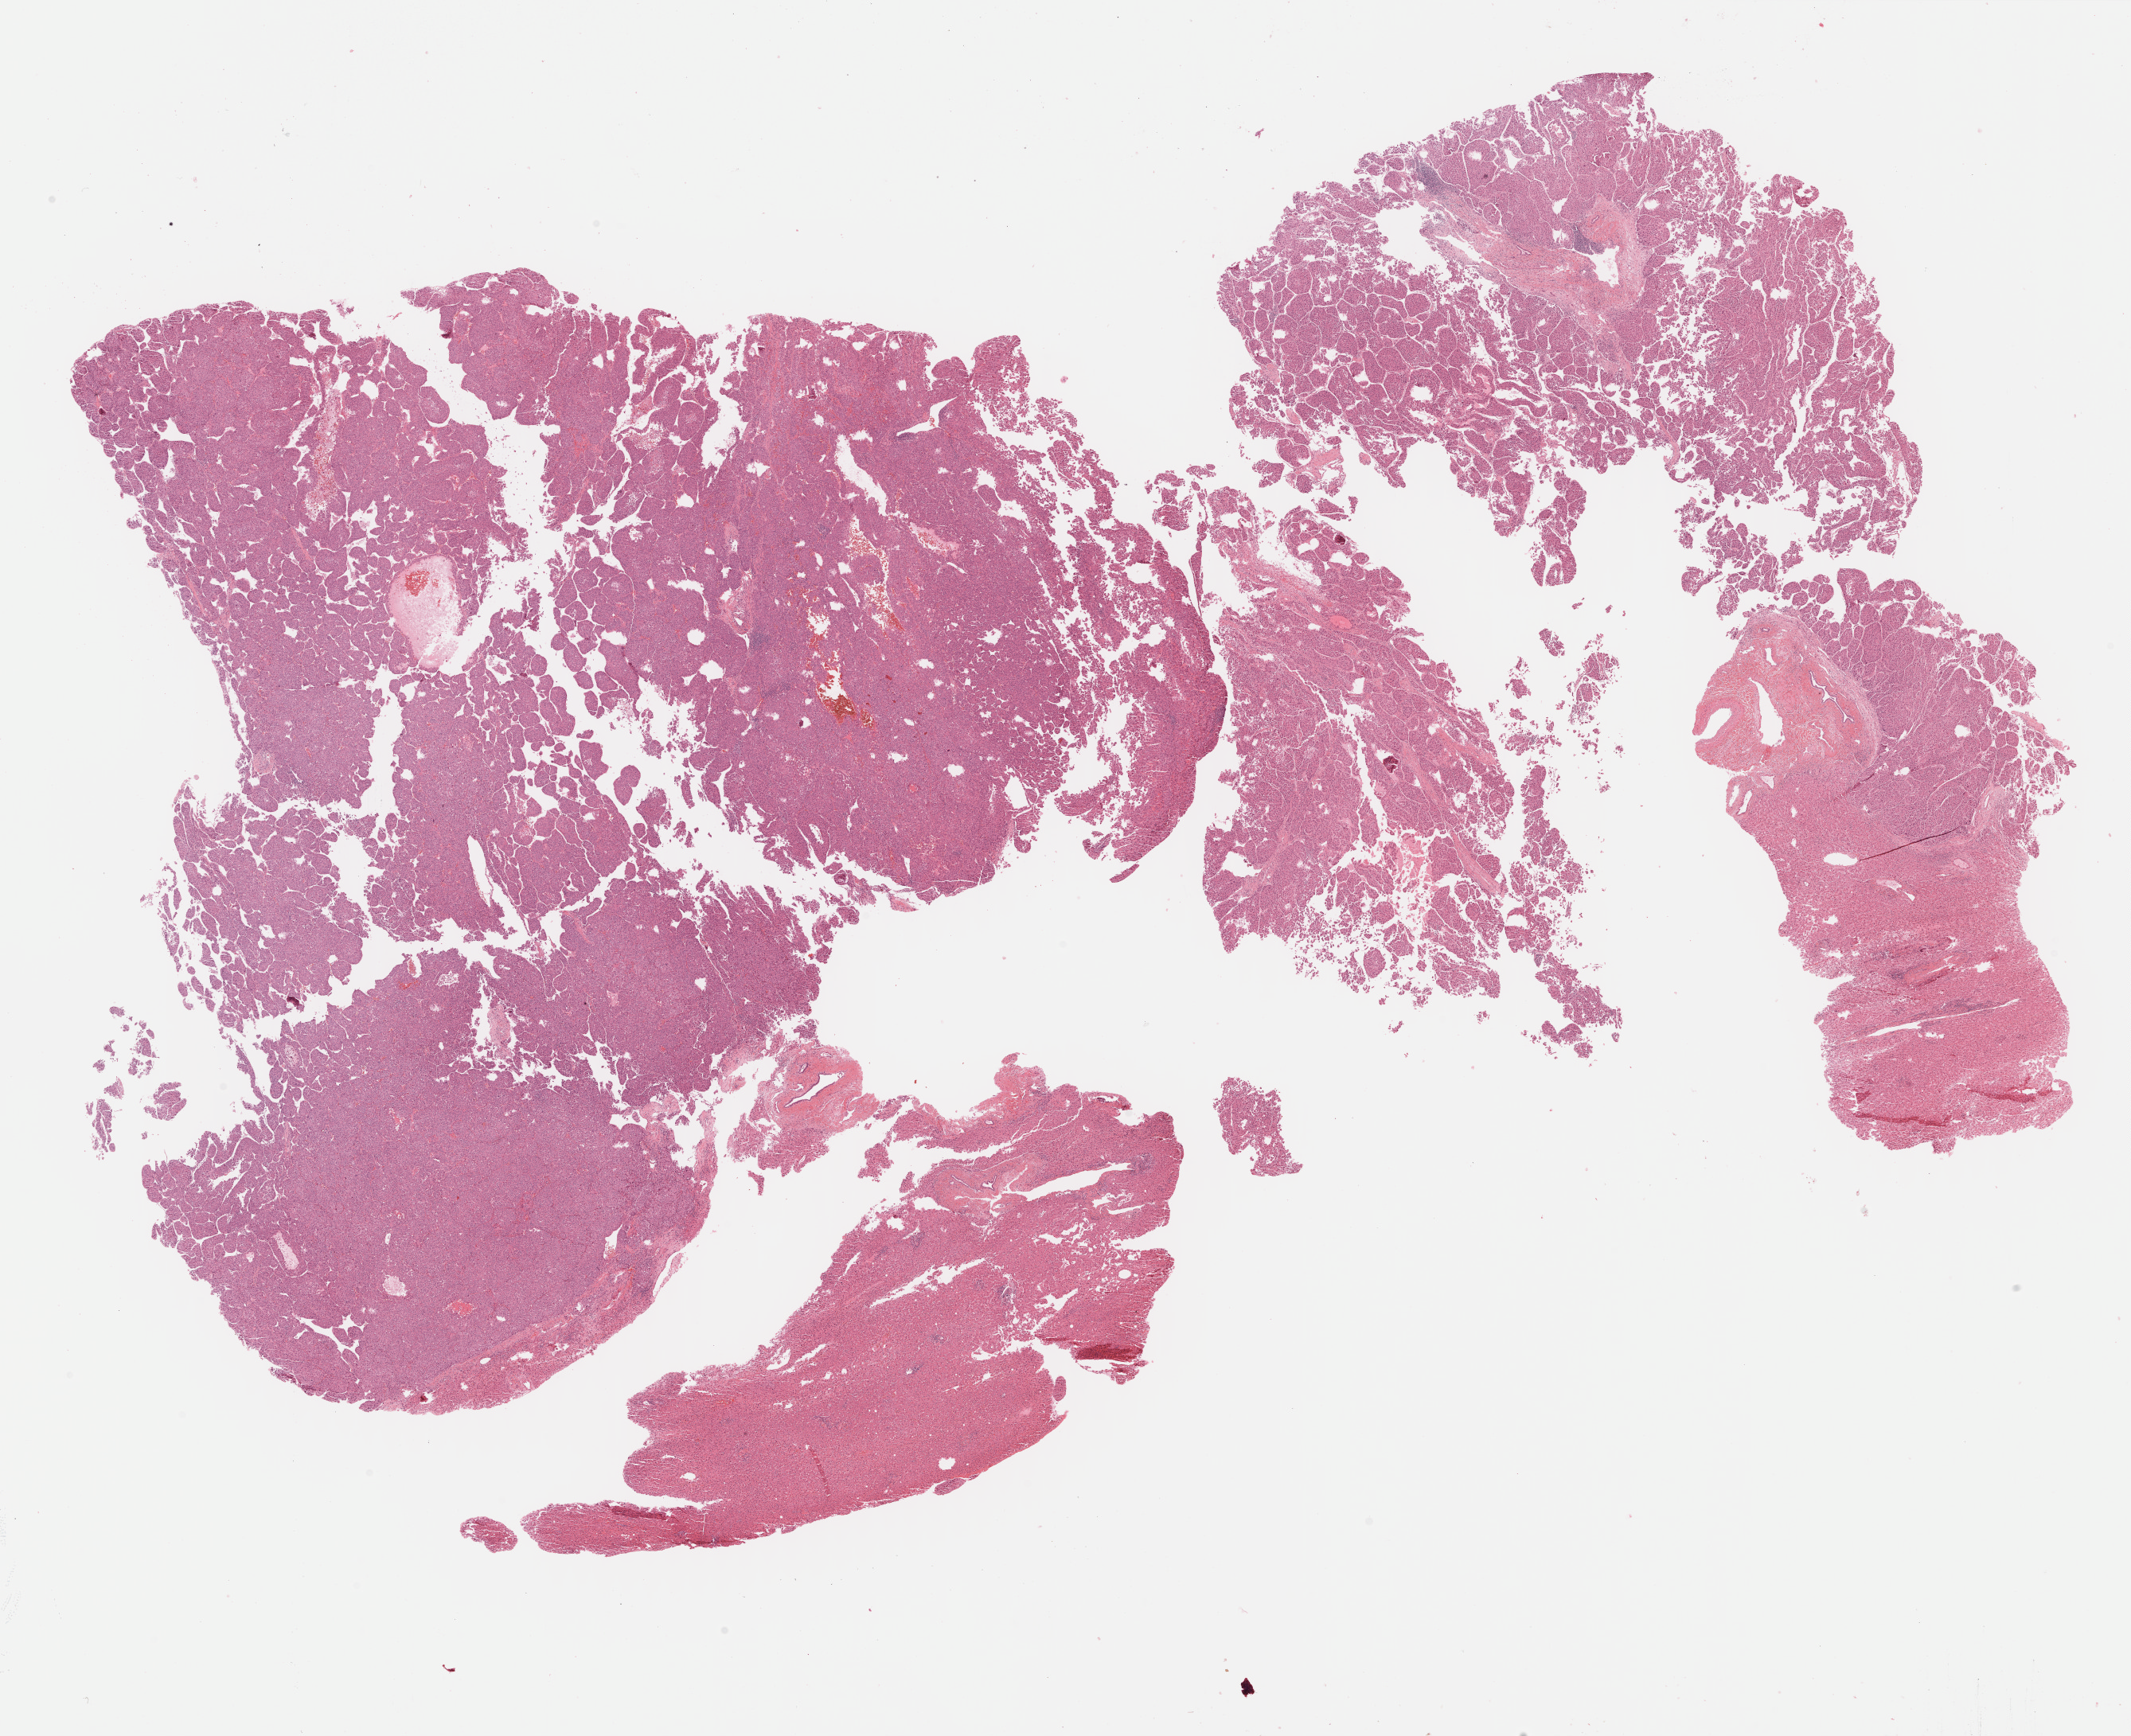
Hematoxylin and eosin (H&E) stained whole-slide image, low-resolution overview of the scanned area, about 21.7 x 17.7 mm (from a 40x scan), formalin-fixed paraffin-embedded (FFPE) diagnostic section, sample: primary tumour, liver. Male, age 67 years at initial diagnosis. Histologic grade: G3 (poorly differentiated).
• AJCC pathologic stage: I
• histologic diagnosis: Hepatocellular carcinoma, NOS